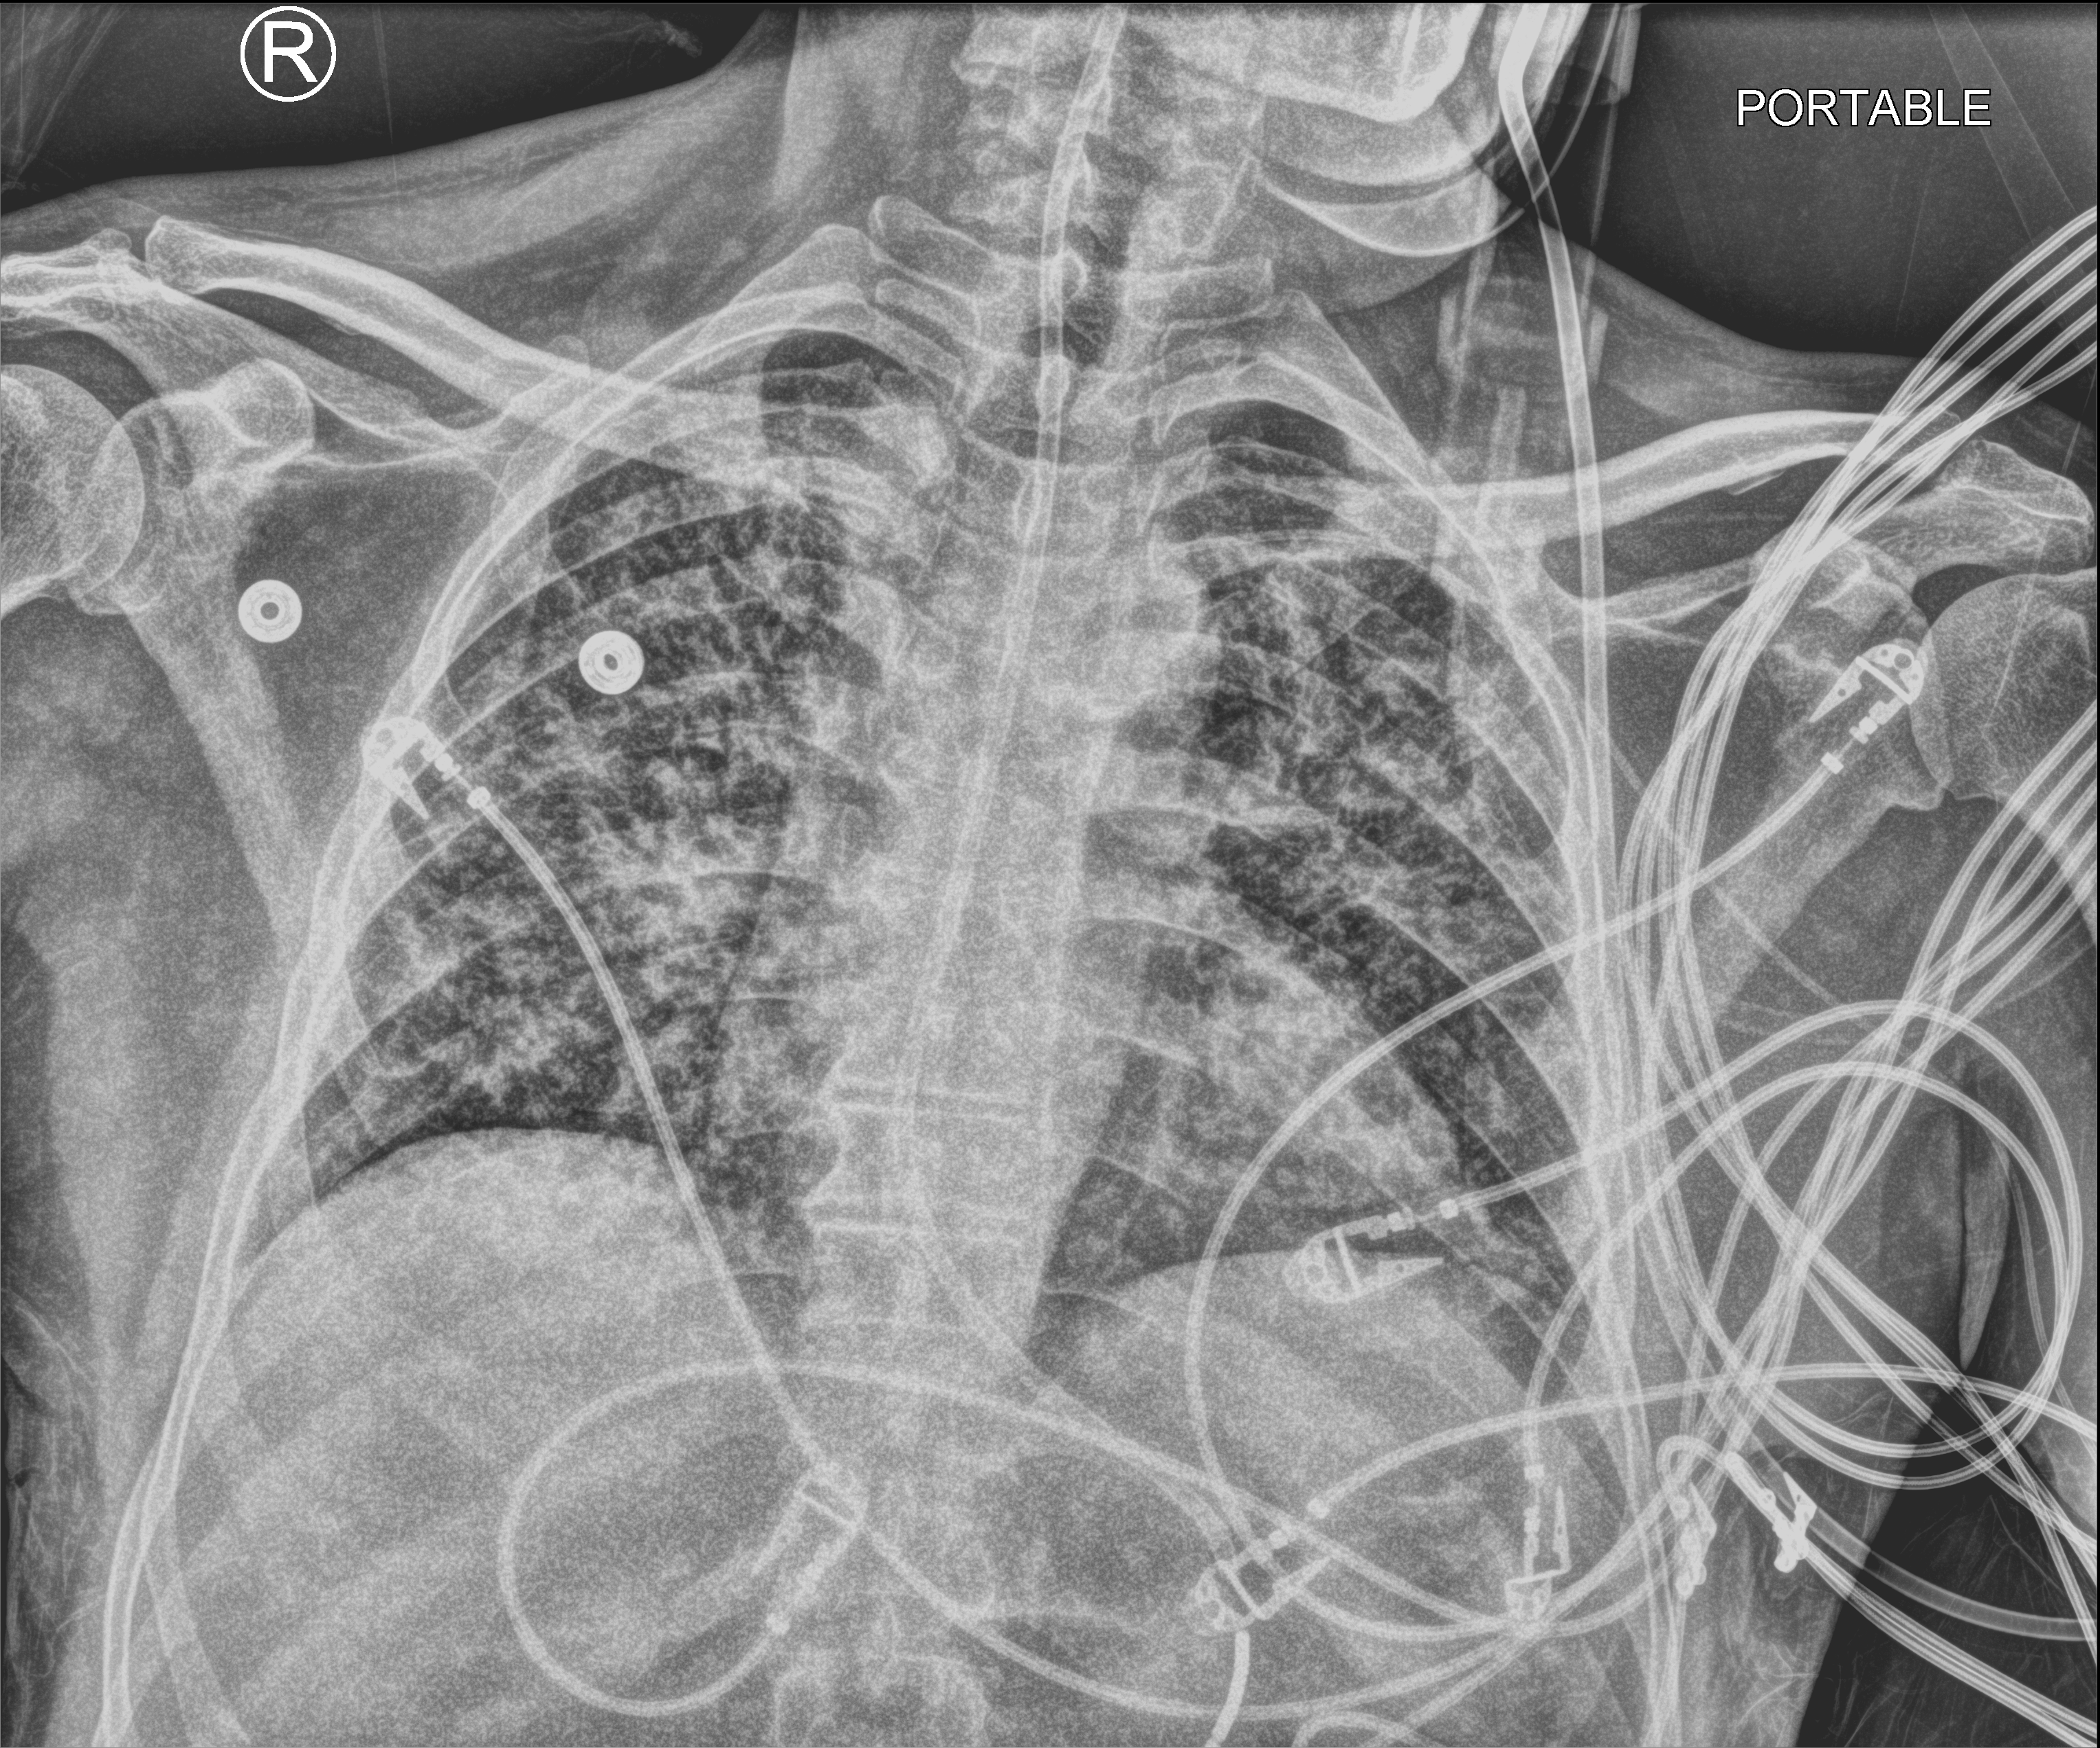
Chest X-ray (portable), anteroposterior (AP) projection. Patient hospitalised with COVID-19; male, aged 18–59 years.
Hospital-stay facts (about this admission, not read from this image; timing relative to this image not recorded): mechanically ventilated during this hospital stay: yes; admitted to intensive care during this hospital stay: yes.